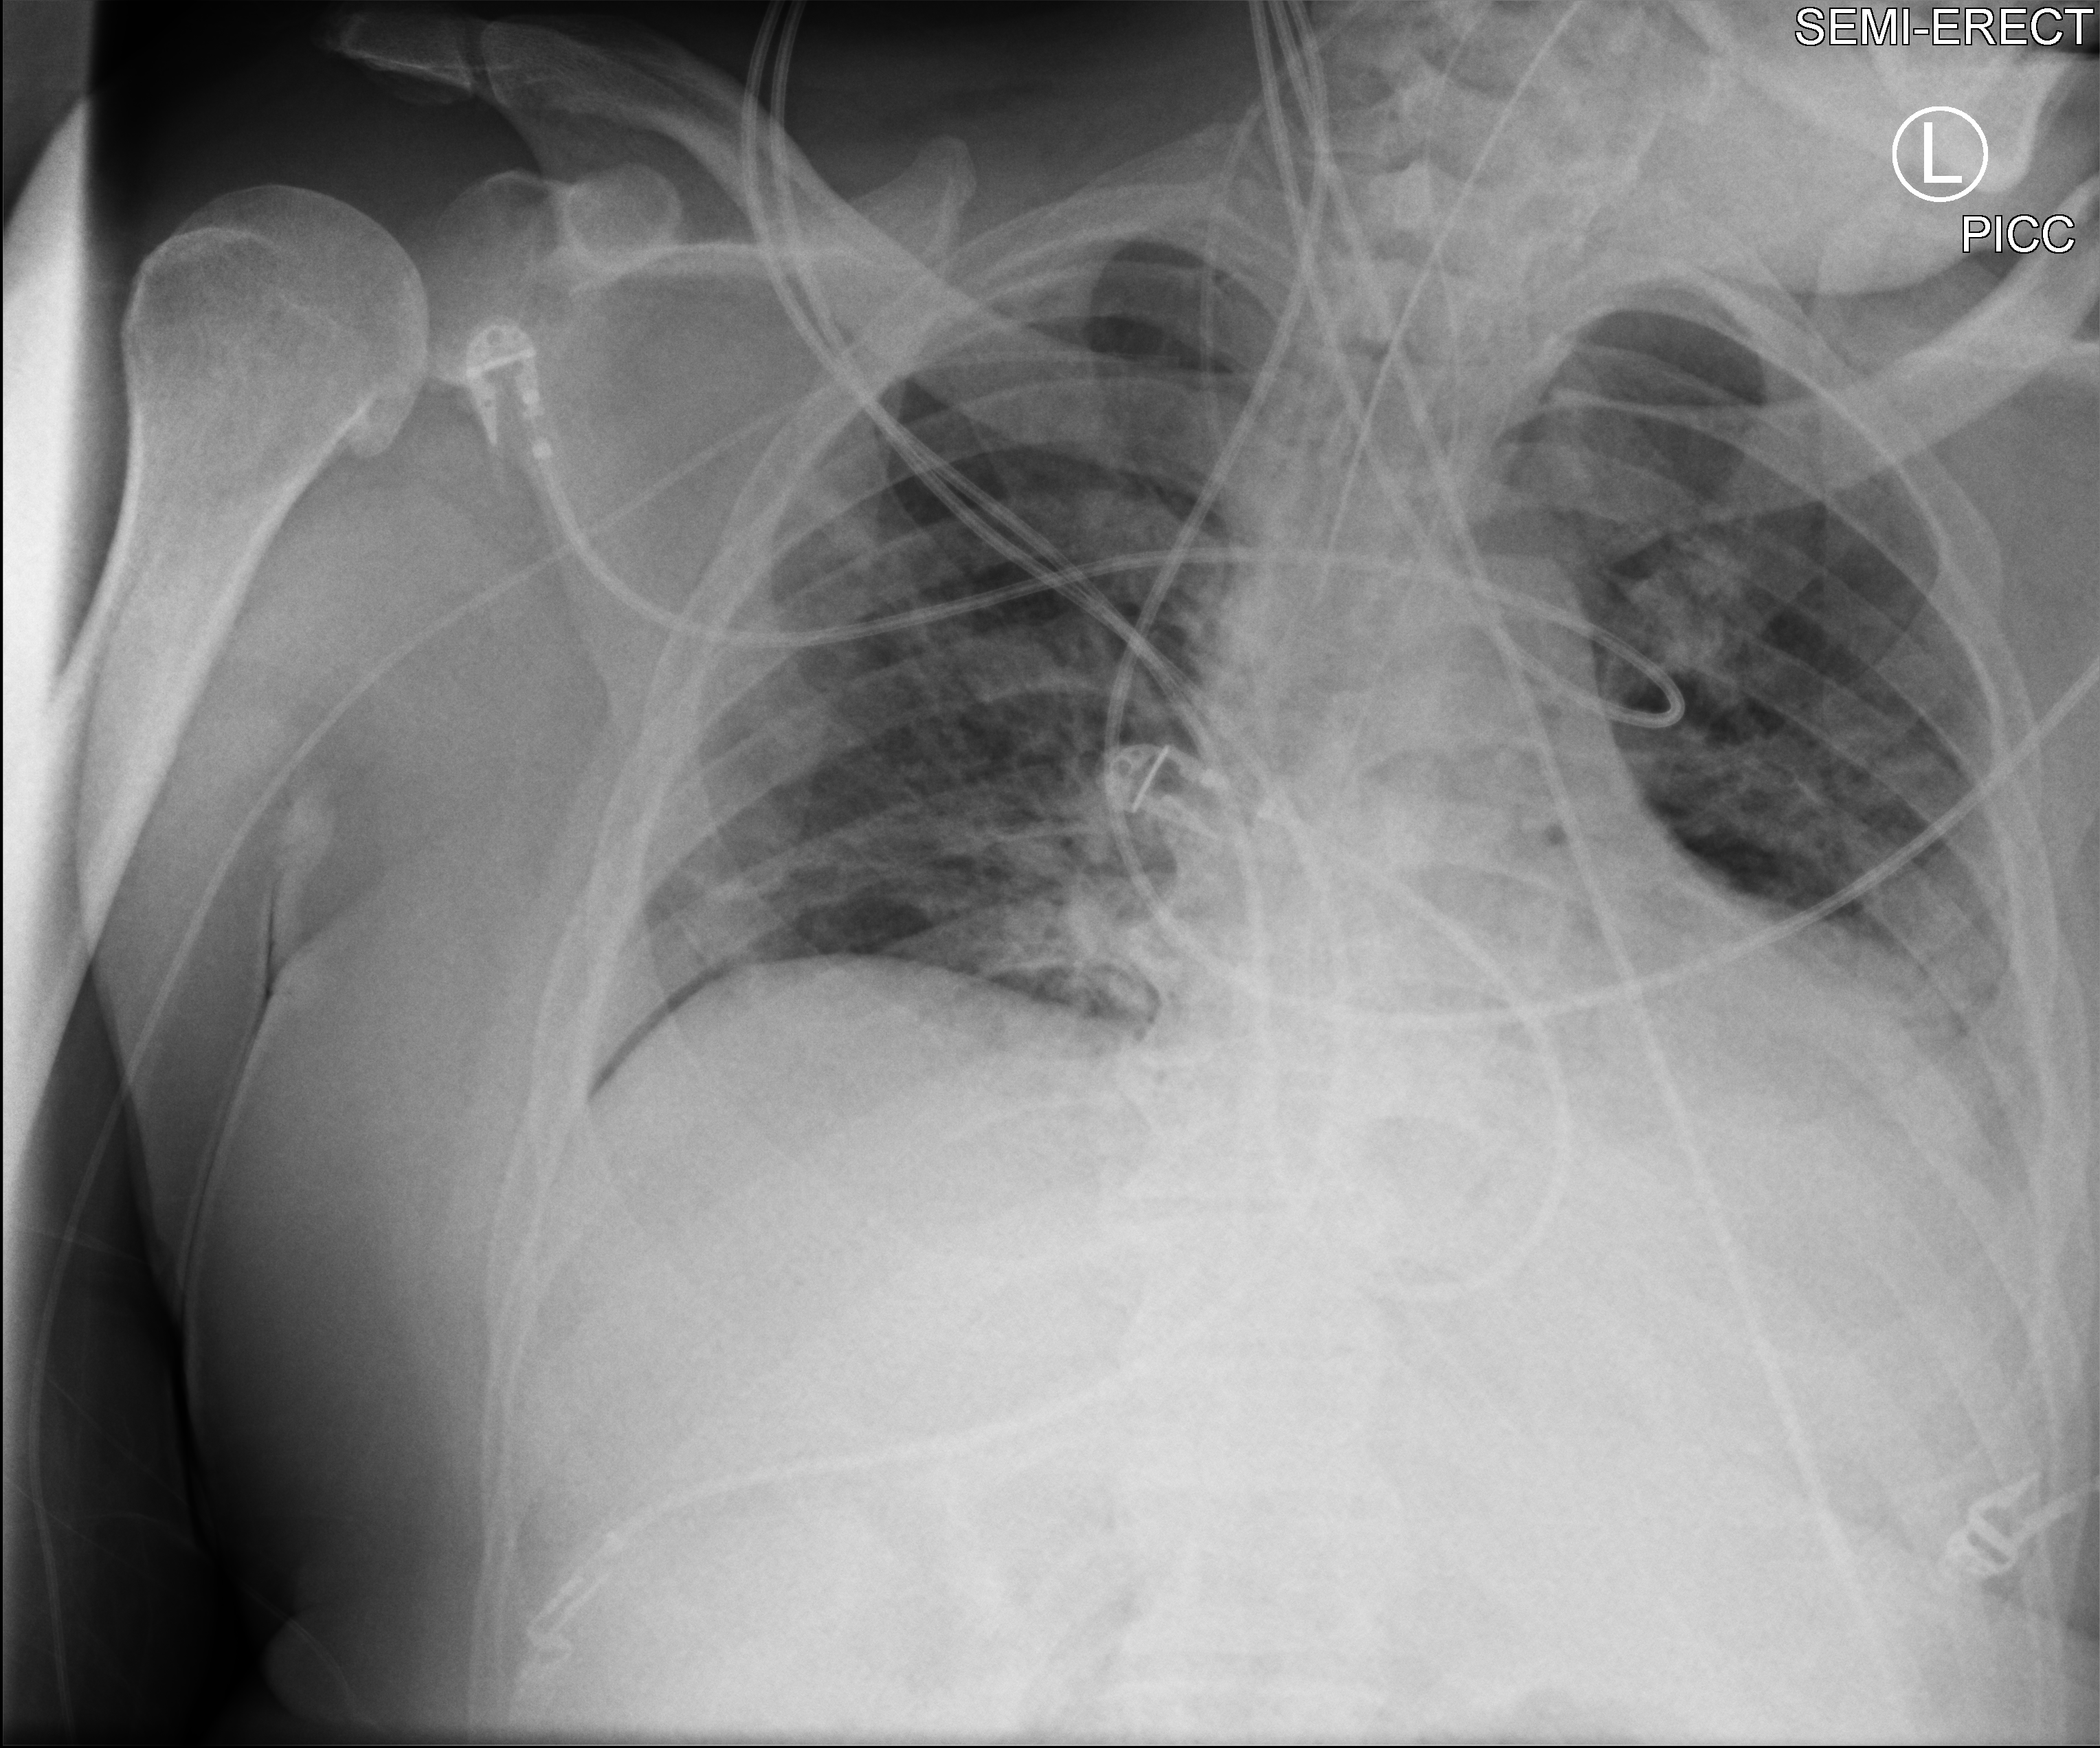
Bedside chest radiograph (computed radiography). Patient hospitalised with COVID-19; male, aged 18–59 years.
Admission-level facts for this patient (not findings on this image; timing relative to this image not recorded):
- mechanically ventilated during this hospital stay: yes
- chronic kidney disease (admission record): no
- diabetes (admission record): no